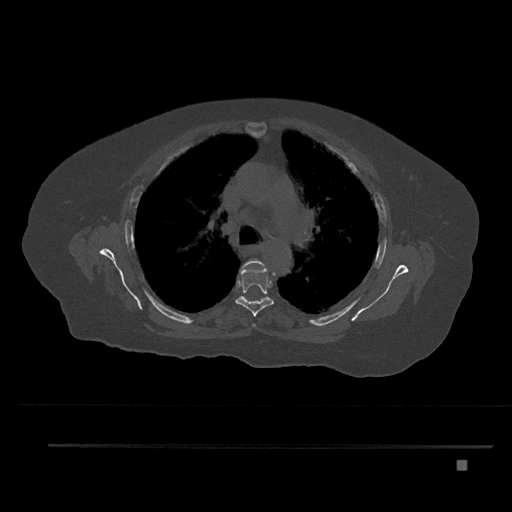
CT including the spine, one axial slice. Position 569 of 797 along the scan axis. Reconstruction kernel Br40s/3. Bone window (W 1800 / L 400 HU). 0.5 mm slice thickness. 512 × 512 image matrix. Patient: female, 76 years. Case-level facts recorded for this patient, not image findings: primary cancer: lung.
Outlined on this slice (semi-automatically segmented with operator editing):
- T4 vertebra: bounding box [x1, y1, x2, y2] px = [241, 258, 264, 327]
- T5 vertebra: [235, 268, 274, 317]
- T6 vertebra: [259, 299, 262, 302]